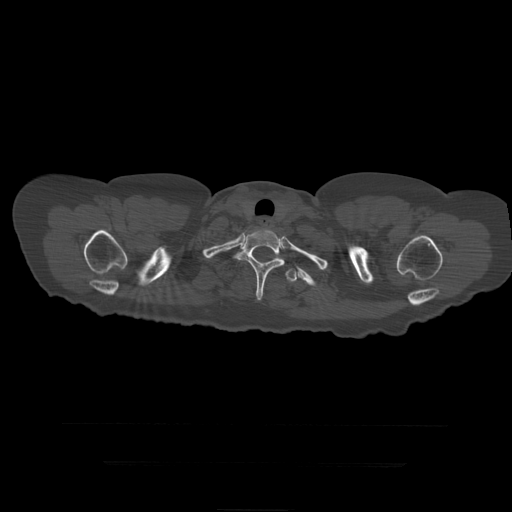
CT including the spine, one axial slice; slice 375 of 399 in the series (ordered by position); reconstruction kernel STANDARD; 120 kVp; bone window (W 1800 / L 400 HU); 1.25 mm slice thickness; 512 × 512 image matrix. Patient age 41 years. Case-level facts recorded for this patient, not image findings: primary cancer: breast.
Structures marked on this image (semi-automatically segmented with operator editing):
- T1 vertebra: bounding box <252,229,267,234> (left, top, right, bottom; pixels)
- T2 vertebra: <233,229,285,301>
- T3 vertebra: <283,259,298,282>